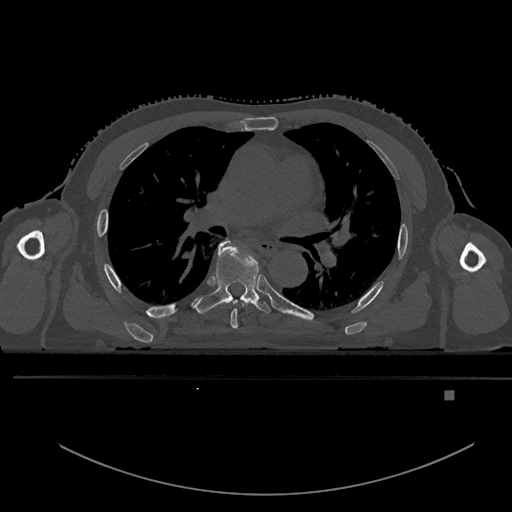
CT including the spine, one axial slice; position 324 of 969 along the scan axis; bone window (W 1800 / L 400 HU); 0.5 mm slice thickness; 512 × 512 image matrix. Male patient, age 82 years. Case-level facts recorded for this patient, not image findings: primary cancer: prostate.
Outlined on this slice (semi-automatic segmentation, software-assisted and operator-edited):
- T5 vertebra: bounding box (x1, y1, x2, y2) in pixels: (227, 238, 252, 329)
- T6 vertebra: (191, 239, 273, 314)